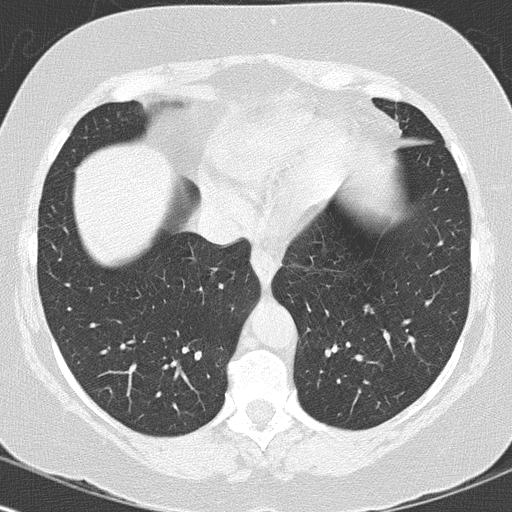
Chest CT (low-dose screening protocol), one axial image, baseline screening round, lung window (W 1500 / L -600 HU), 2 mm slice thickness, lung (sharp) reconstruction kernel (B50f), slice 100 of 144 in the series. Female, age 60 years at enrolment. Former smoker at enrolment.
• Expert-annotated lung lesion, bounding box <349,289,392,333> (left, top, right, bottom; pixels).
• Reader record for this screening exam (exam-level; its link to the box is not recorded): non-calcified nodule or mass ≥4 mm, left lower lobe, 12 × 10 mm, smooth margins, soft tissue attenuation.
• Official screen result: positive, change unspecified: nodule(s) >= 4 mm or enlarging nodule(s), mass(es), or other non-specific abnormalities suspicious for lung cancer.
• Participant outcome: lung cancer diagnosed 109 days after this screen — carcinoid tumor, NOS, left lower lobe, carcinoid, stage not assessed, 13 mm at pathology.